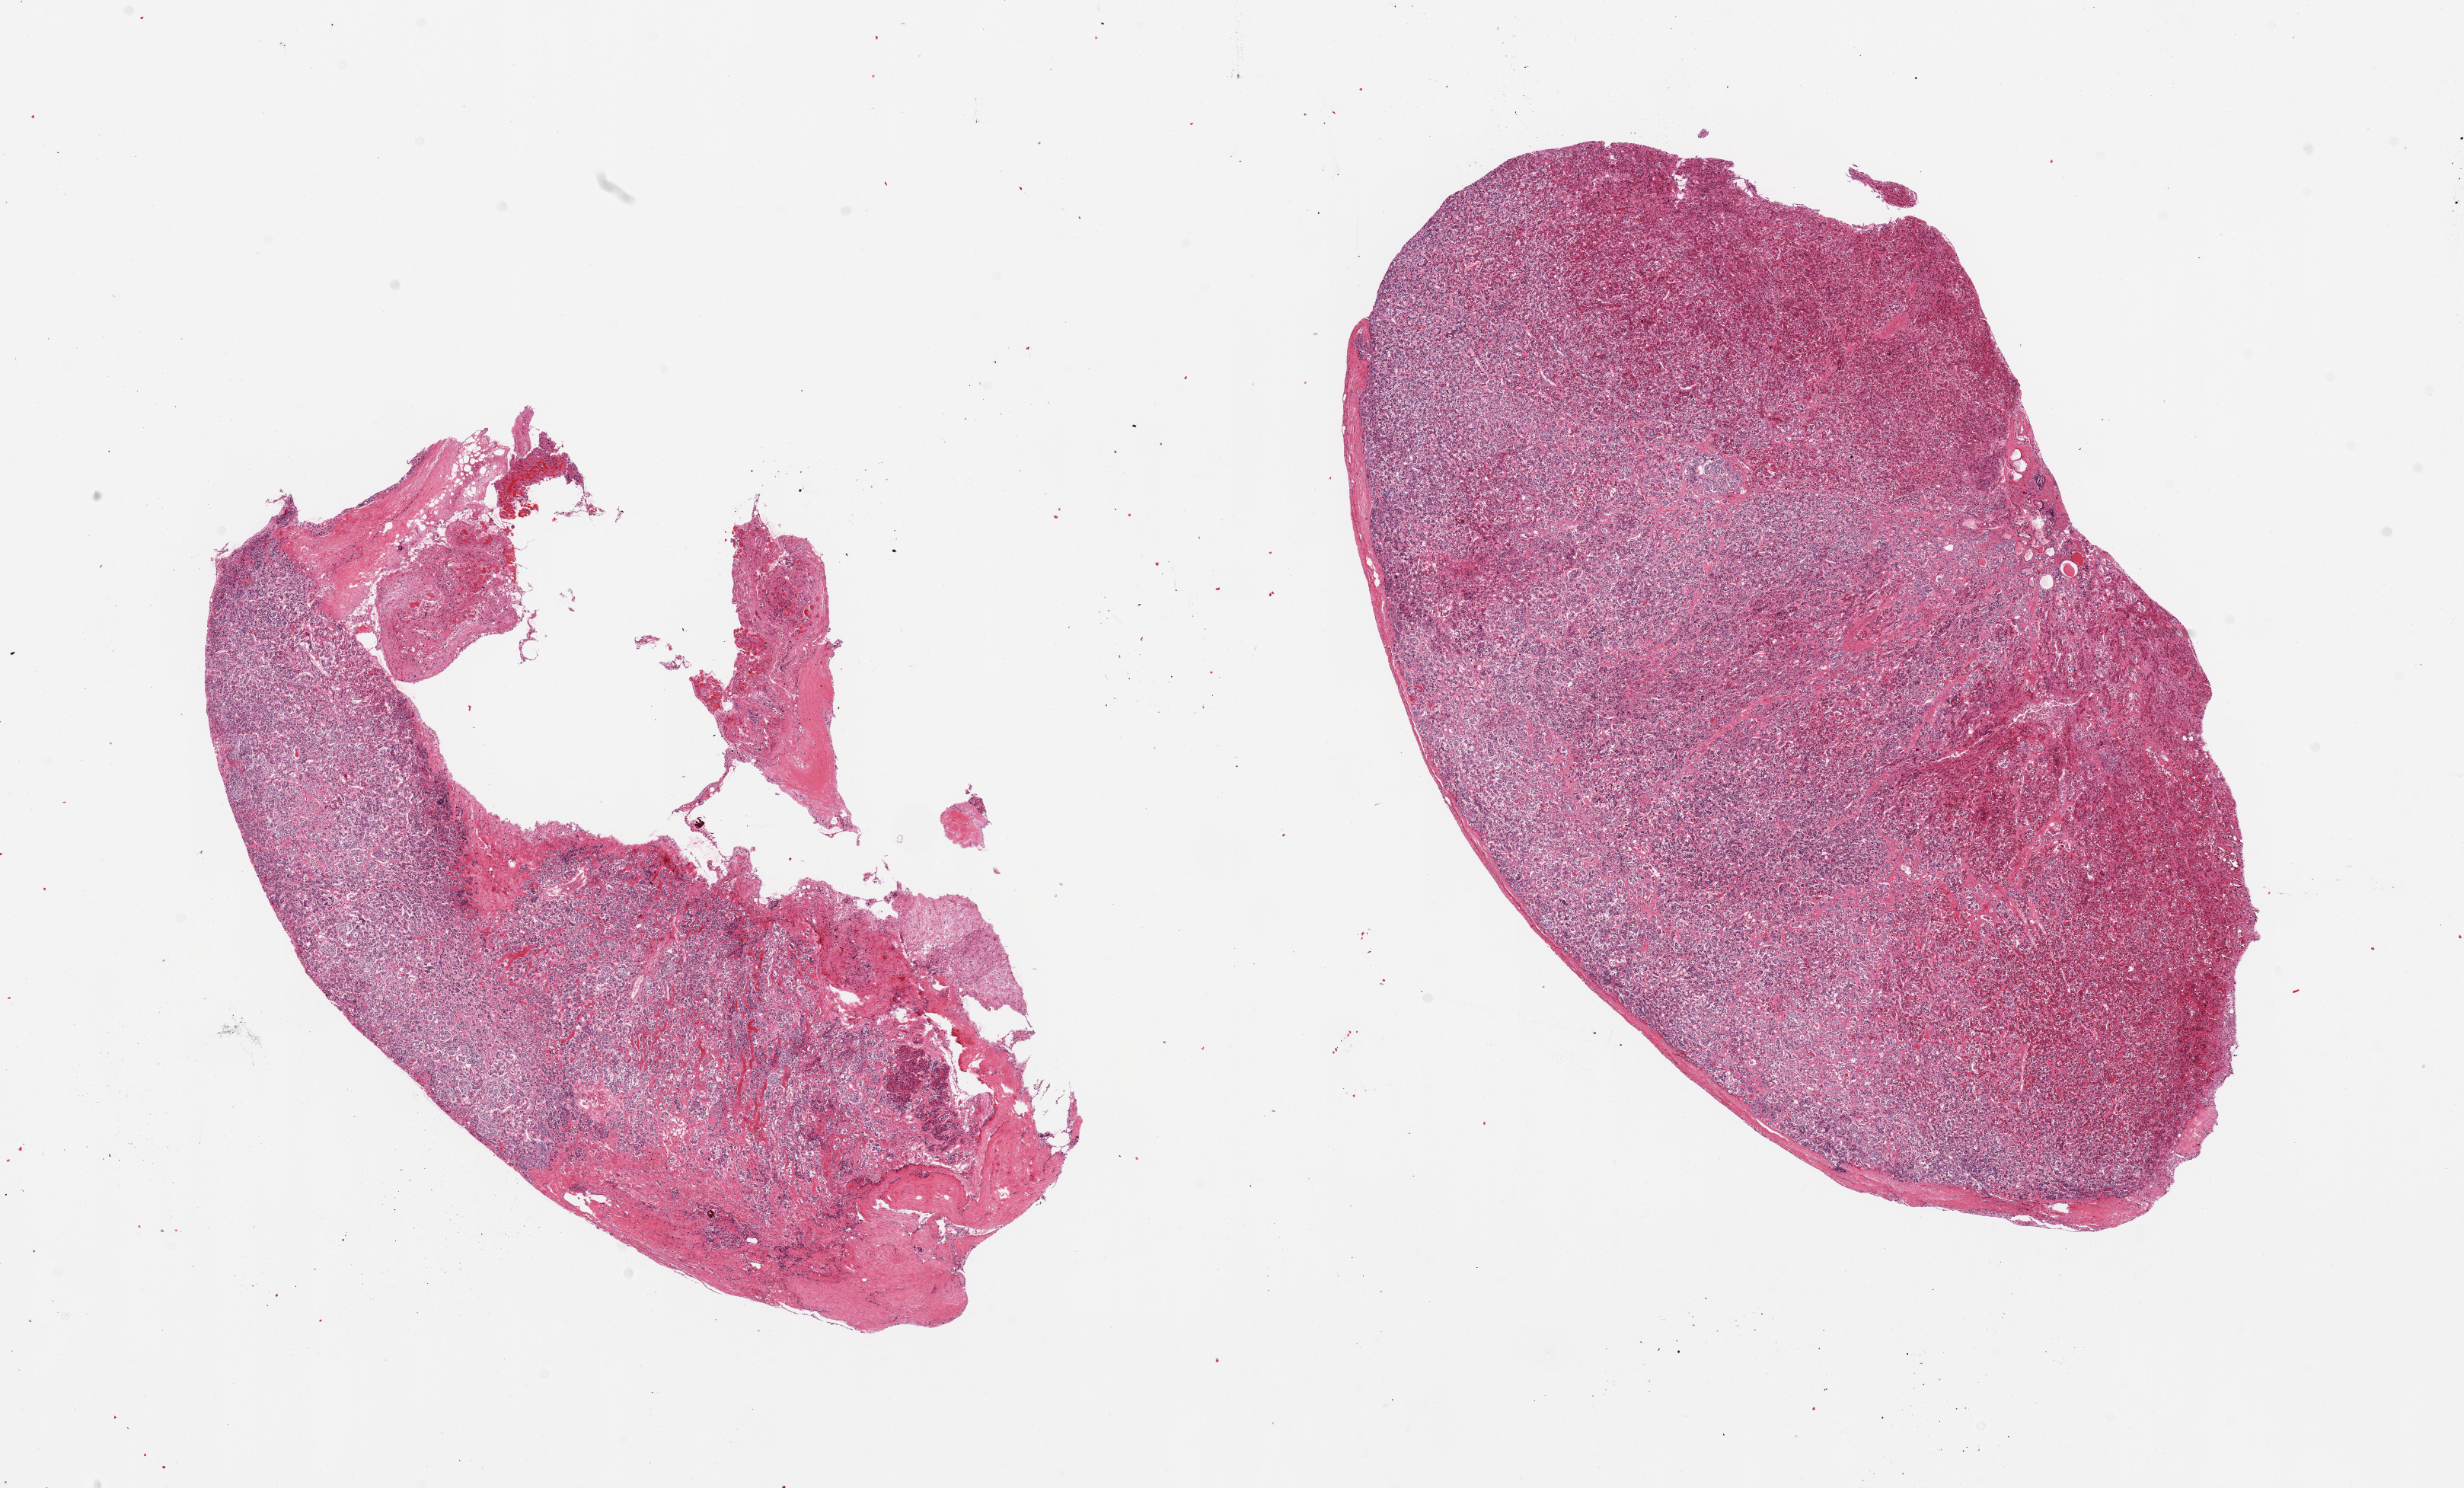
Digitized H&E-stained section, a low-resolution overview of the entire scanned area, about 25.6 x 15.5 mm, PAXgene-fixed paraffin-embedded (PFPE) section, sampled site (target tissue): pituitary, tissue donor sample. Female donor.
• review note (as recorded): 2 pieces, all adenohypophysis